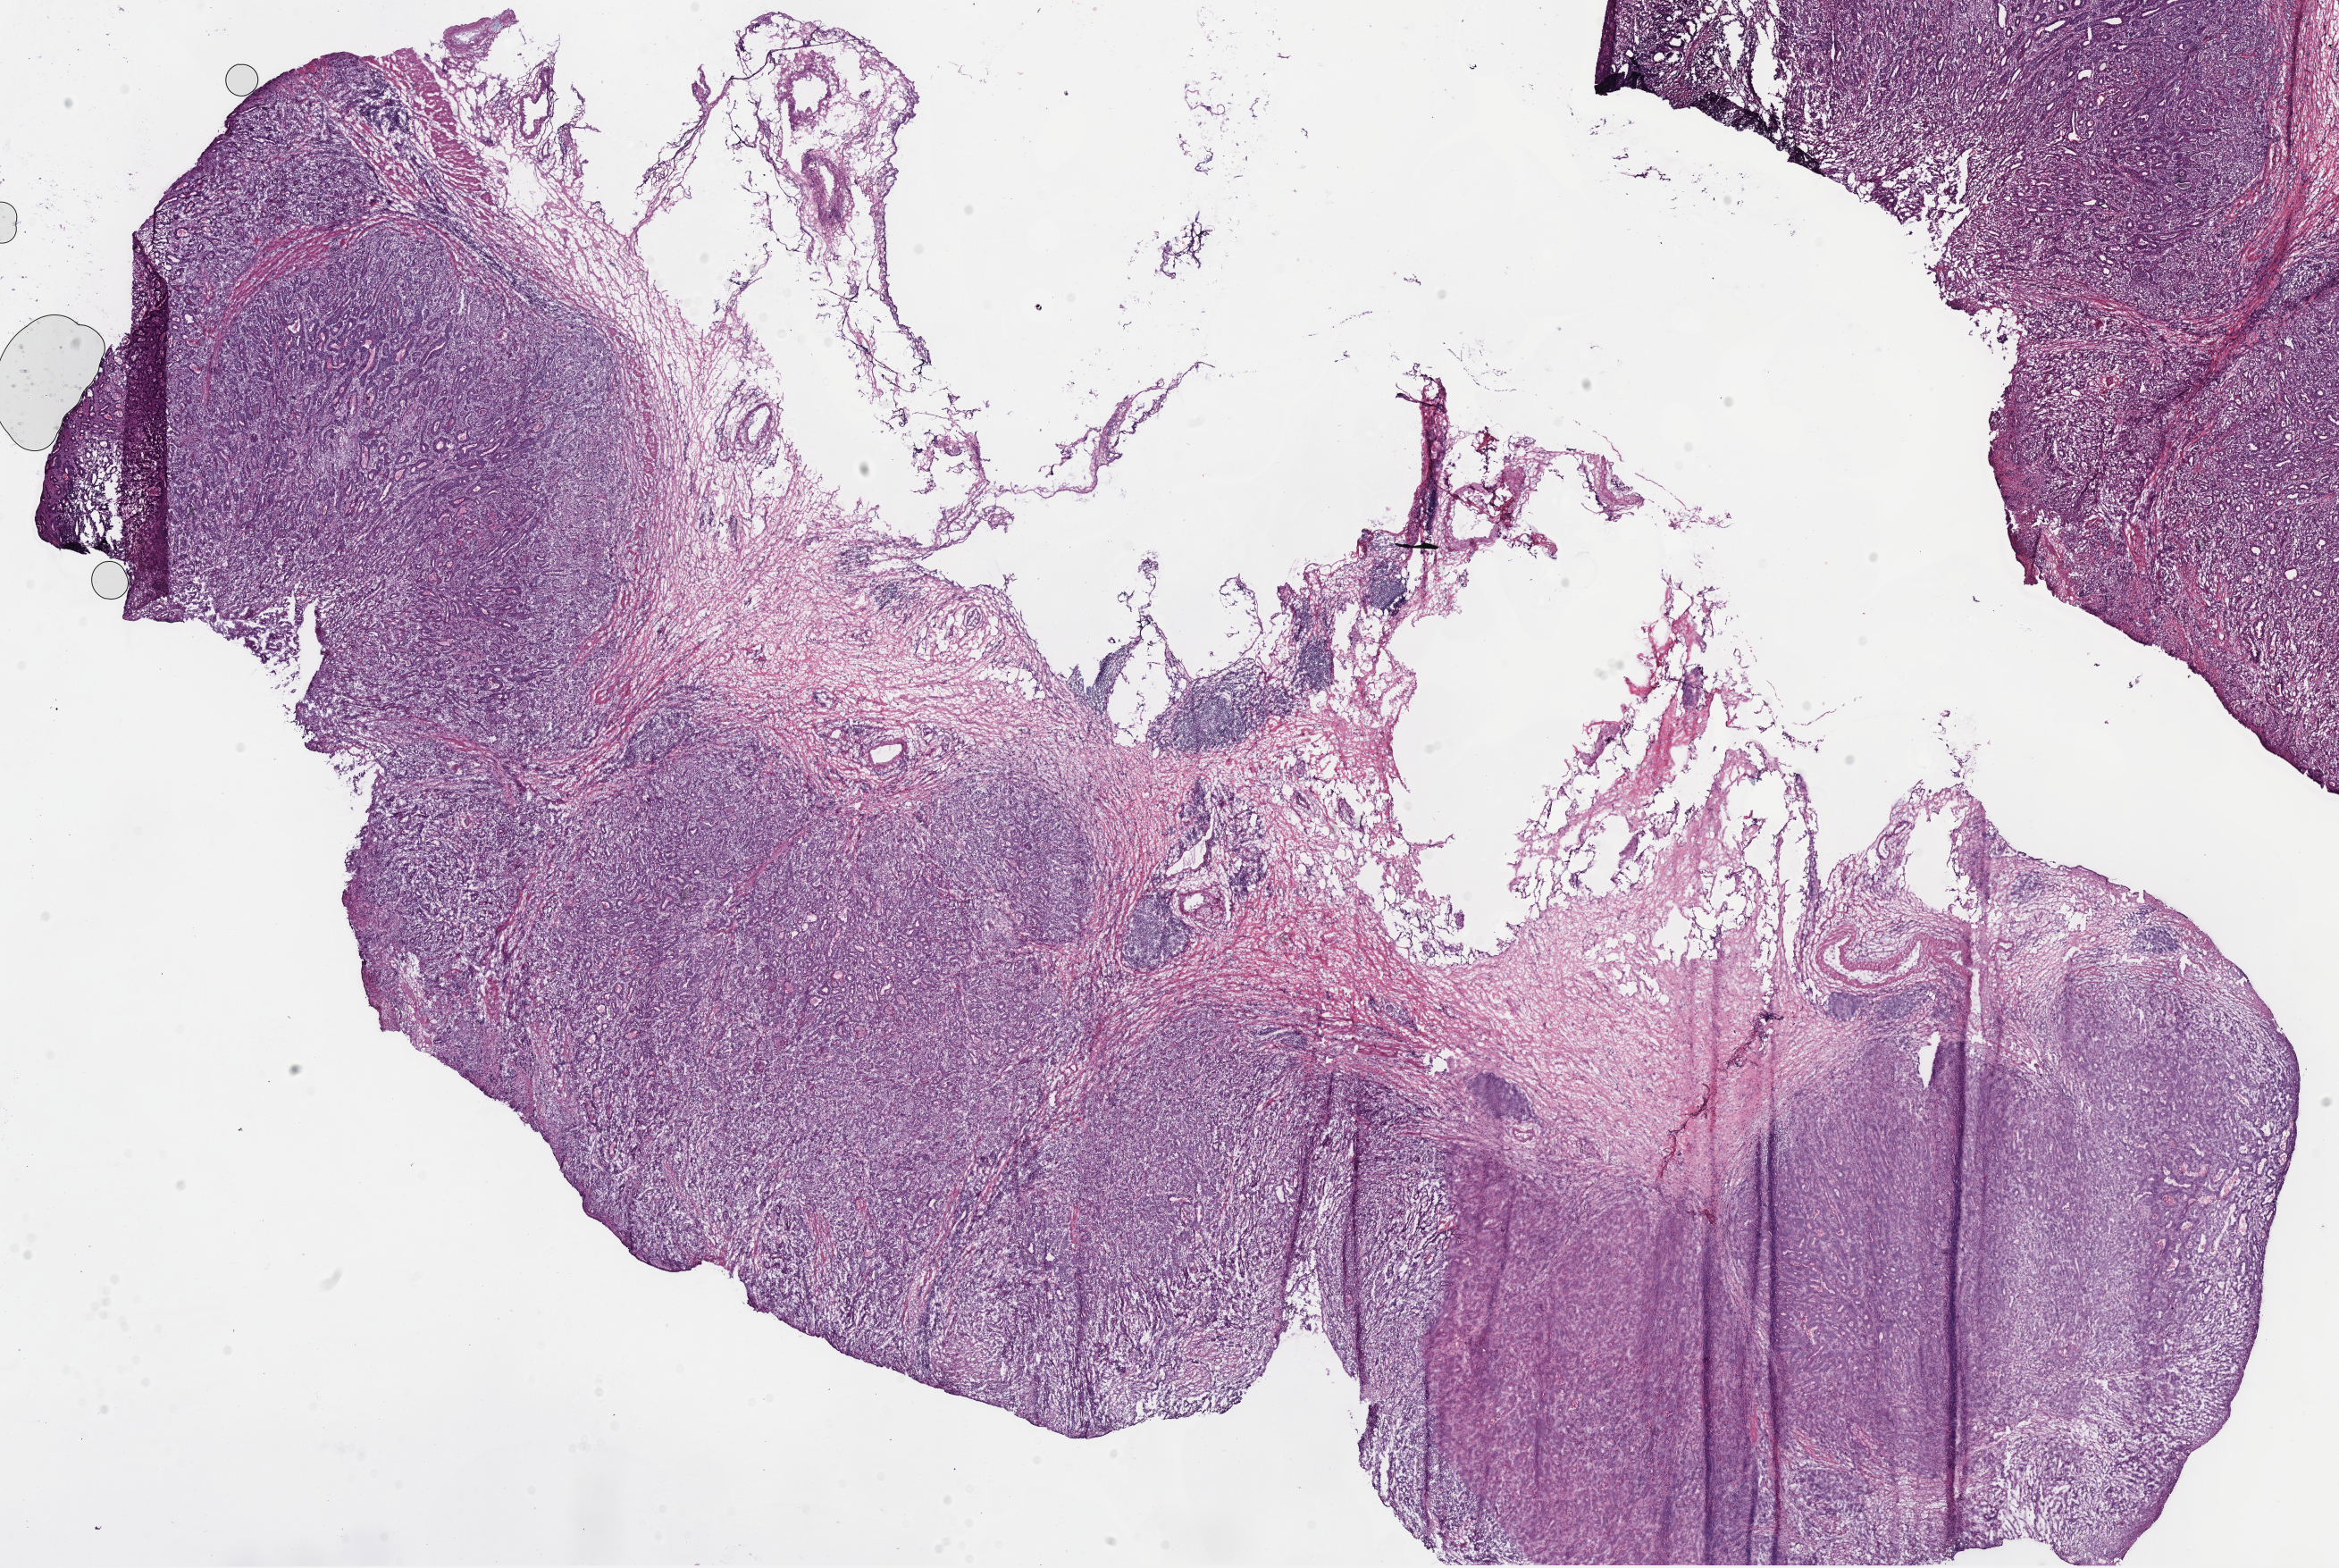
Whole-slide histology image, H&E — shown as a low-resolution overview of the whole scanned area (about 20.6 x 13.8 mm, slide scanned at 40x); frozen section; sample: primary tumour, stomach. Female, age 71 years at initial diagnosis. Histologic grade: G2 (moderately differentiated). Pathologist review of this section (percent, as recorded): tumour cells 84%, tumour nuclei 85%, normal cells 0%, stromal cells 15%, necrosis 1%. Inflammatory infiltration, as recorded: lymphocyte infiltration 5%, monocyte infiltration 2%, neutrophil infiltration 5%.
• AJCC pathologic stage: IIB (7th edition)
• lymph nodes positive (case pathology): 0 of 5 examined
• pathologic diagnosis: Adenocarcinoma, NOS (body of stomach)